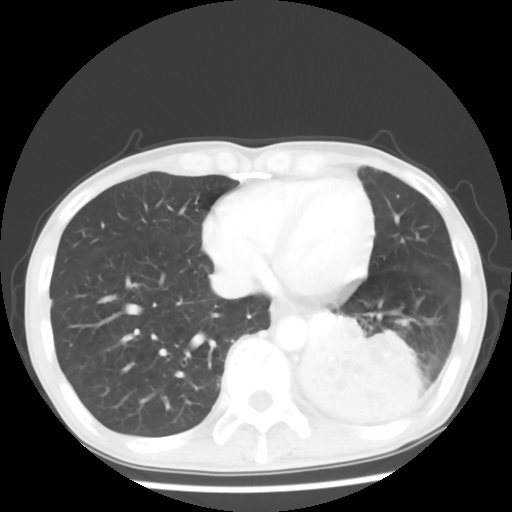
Chest CT, one axial slice. Position 18 of 64 along the scan axis. Reconstruction kernel STANDARD. 120 kVp. Lung window (W 1500 / L -600 HU). 5 mm slice thickness. 512 × 512 image matrix. Male patient, age 68 years. From the clinical record (not read from this slice): clinical TNM (as recorded): T4 N0 M0.
Outlined on this slice (bounding box drawn by a radiologist):
- lung tumour (recorded histology: squamous cell carcinoma): box from (x=303, y=303) to (x=413, y=428) px